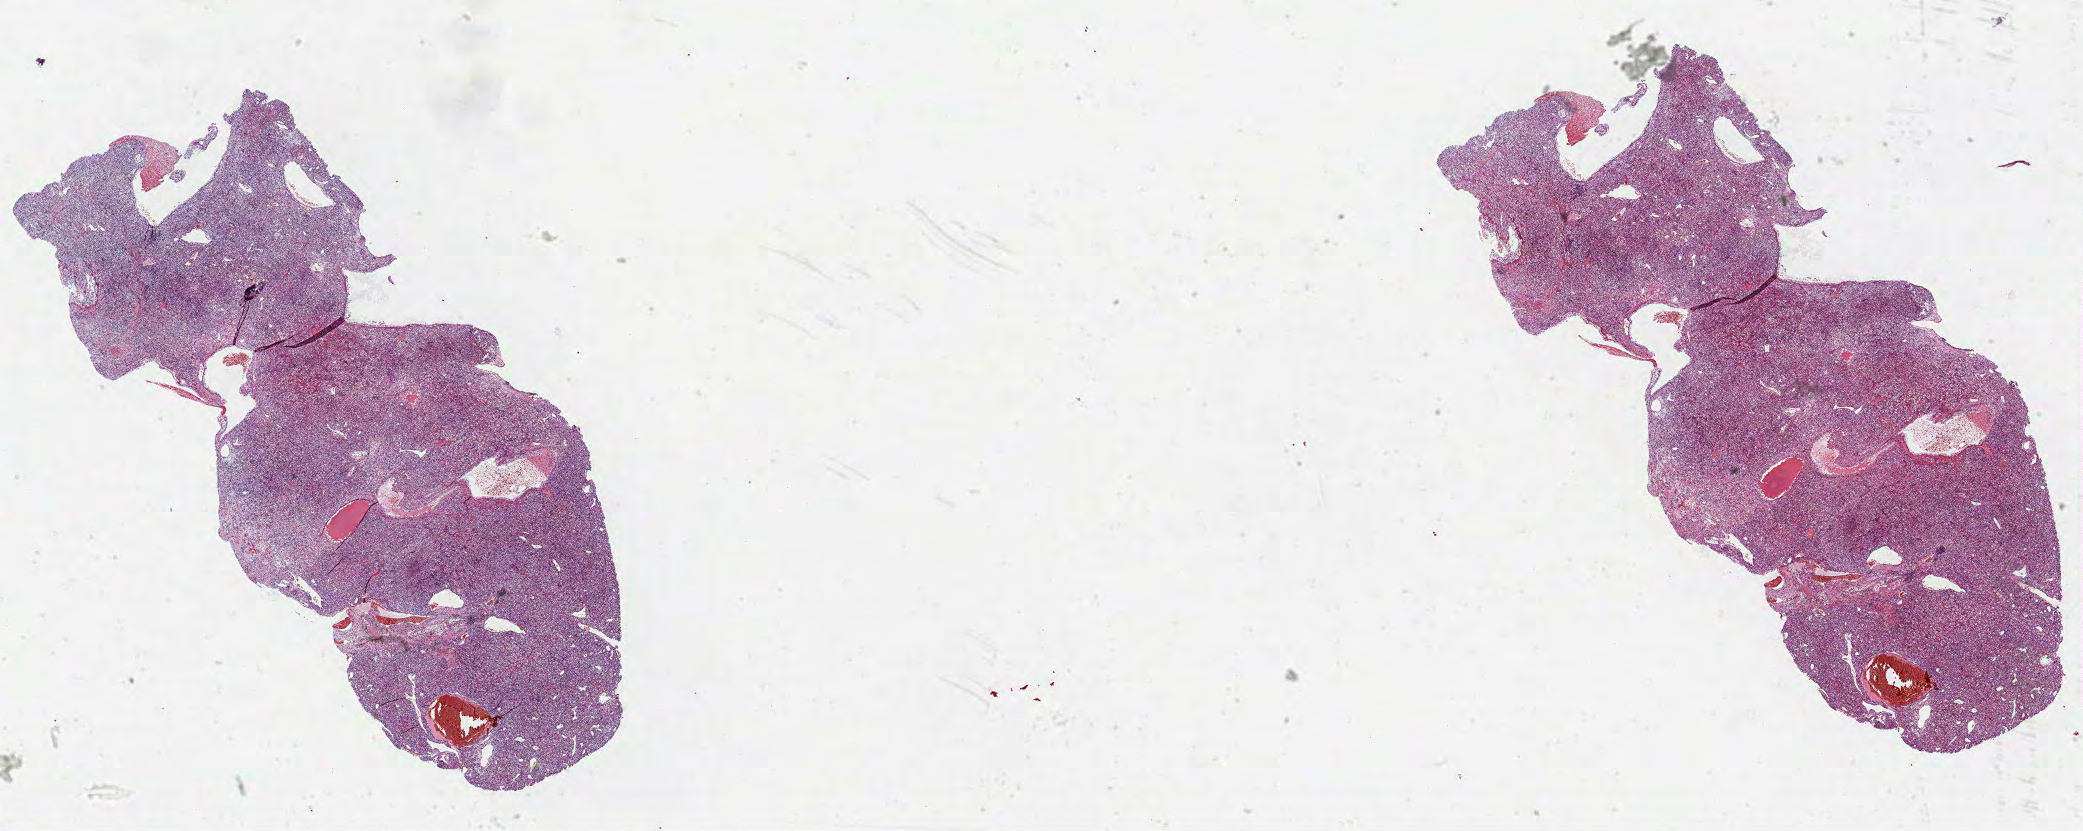
Whole-slide histology image, H&E-stained — whole scanned area (about 33.6 x 13.4 mm, from a 40x scan) shown as a low-resolution overview, FFPE section, primary tumour sample from the kidney. Male patient; age at initial diagnosis 46 years.
Histologic diagnosis: Clear cell adenocarcinoma, NOS.